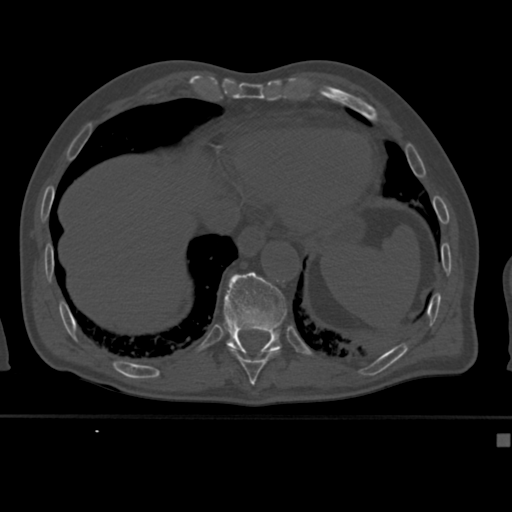
CT including the spine, one axial slice. Slice 220 of 430 in the series (ordered by position). 120 kVp. Bone window (W 1800 / L 400 HU). 1.5 mm slice thickness. 512 × 512 image matrix, field of view 337 × 337 mm. Male patient, age 64 years. Case-level facts recorded for this patient, not image findings: primary cancer: uterus; vertebrae with lytic lesions (as recorded): T1, T4, T5, T7, L5.
Outlined on this slice (semi-automatically segmented with operator editing):
- T10 vertebra: box from (x=229, y=348) to (x=279, y=382) px
- T11 vertebra: (x=223, y=272)–(x=287, y=356)